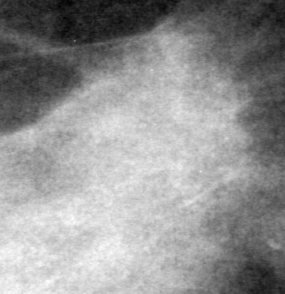
Cropped region of a digitized screen-film mammogram centred on a radiologist-marked abnormality; left breast; MLO view.
Marked abnormality: mass, shape irregular, margins ill defined; BI-RADS assessment category 4; subtlety rating 2 on a 1 (subtle) to 5 (obvious) scale; pathology result (as recorded, not read from the image): malignant.